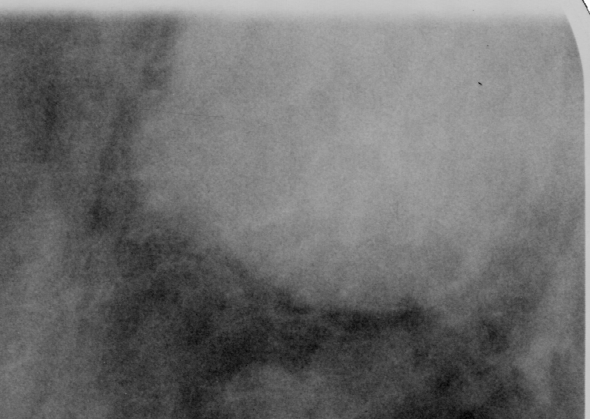
Crop from a digitized film mammogram around one marked abnormality, right breast, MLO view.
Finding: mass, shape round, margins circumscribed; BI-RADS assessment category 5; pathology result (as recorded, not read from the image): malignant.